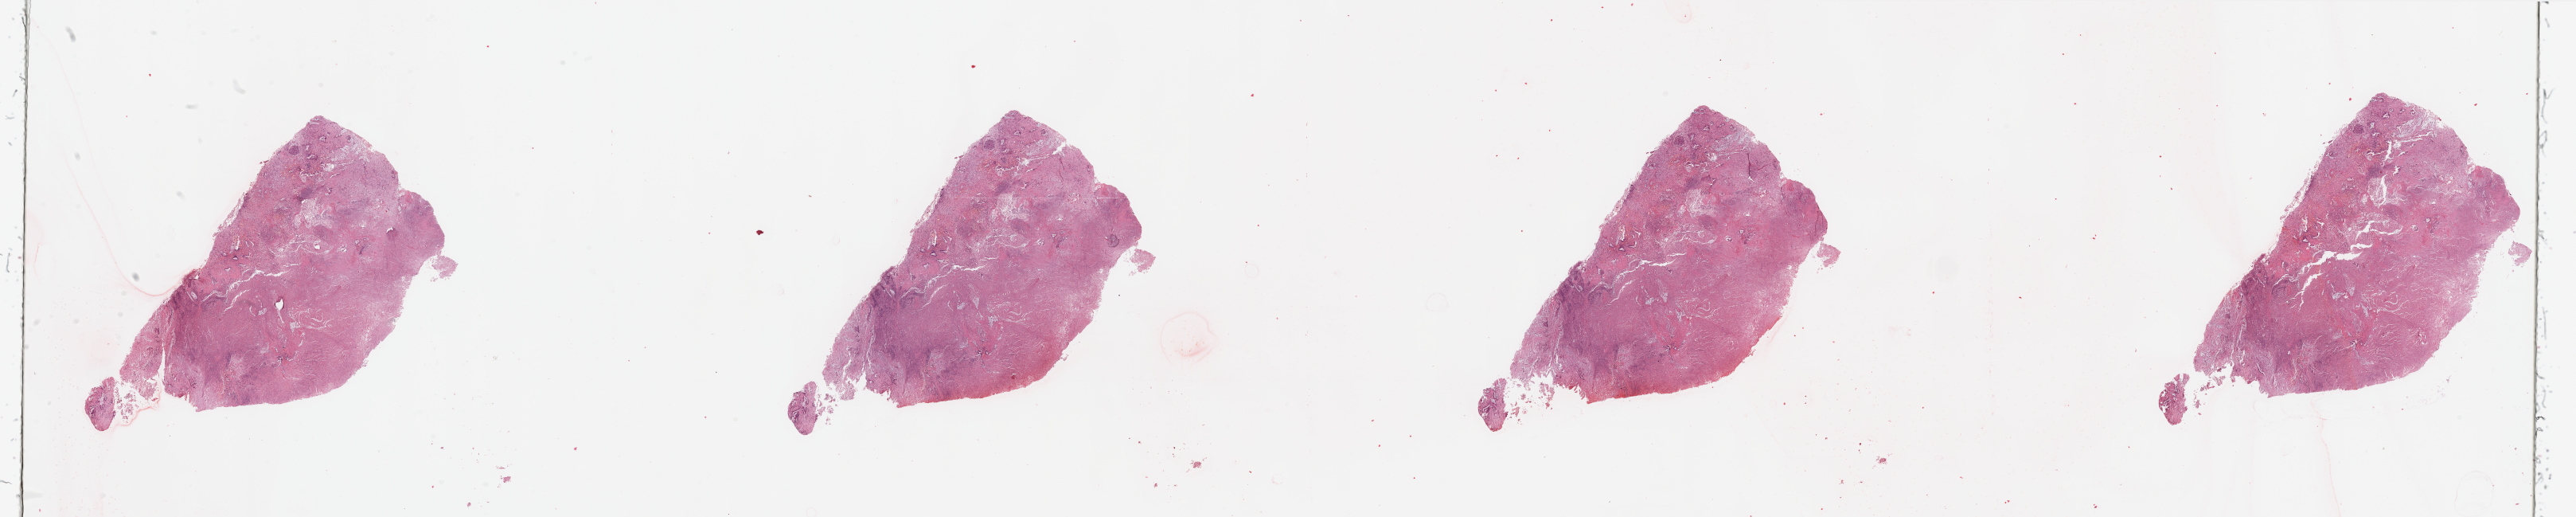
H&E whole-slide image, shown as a low-resolution overview of the whole scanned area (about 51.2 x 10.3 mm). Pancreas, tumour tissue. Patient: male, age 72 years. Histologic grade: G2 (moderately differentiated).
AJCC pathologic stage: IB. Diagnosis: Infiltrating duct carcinoma, NOS.